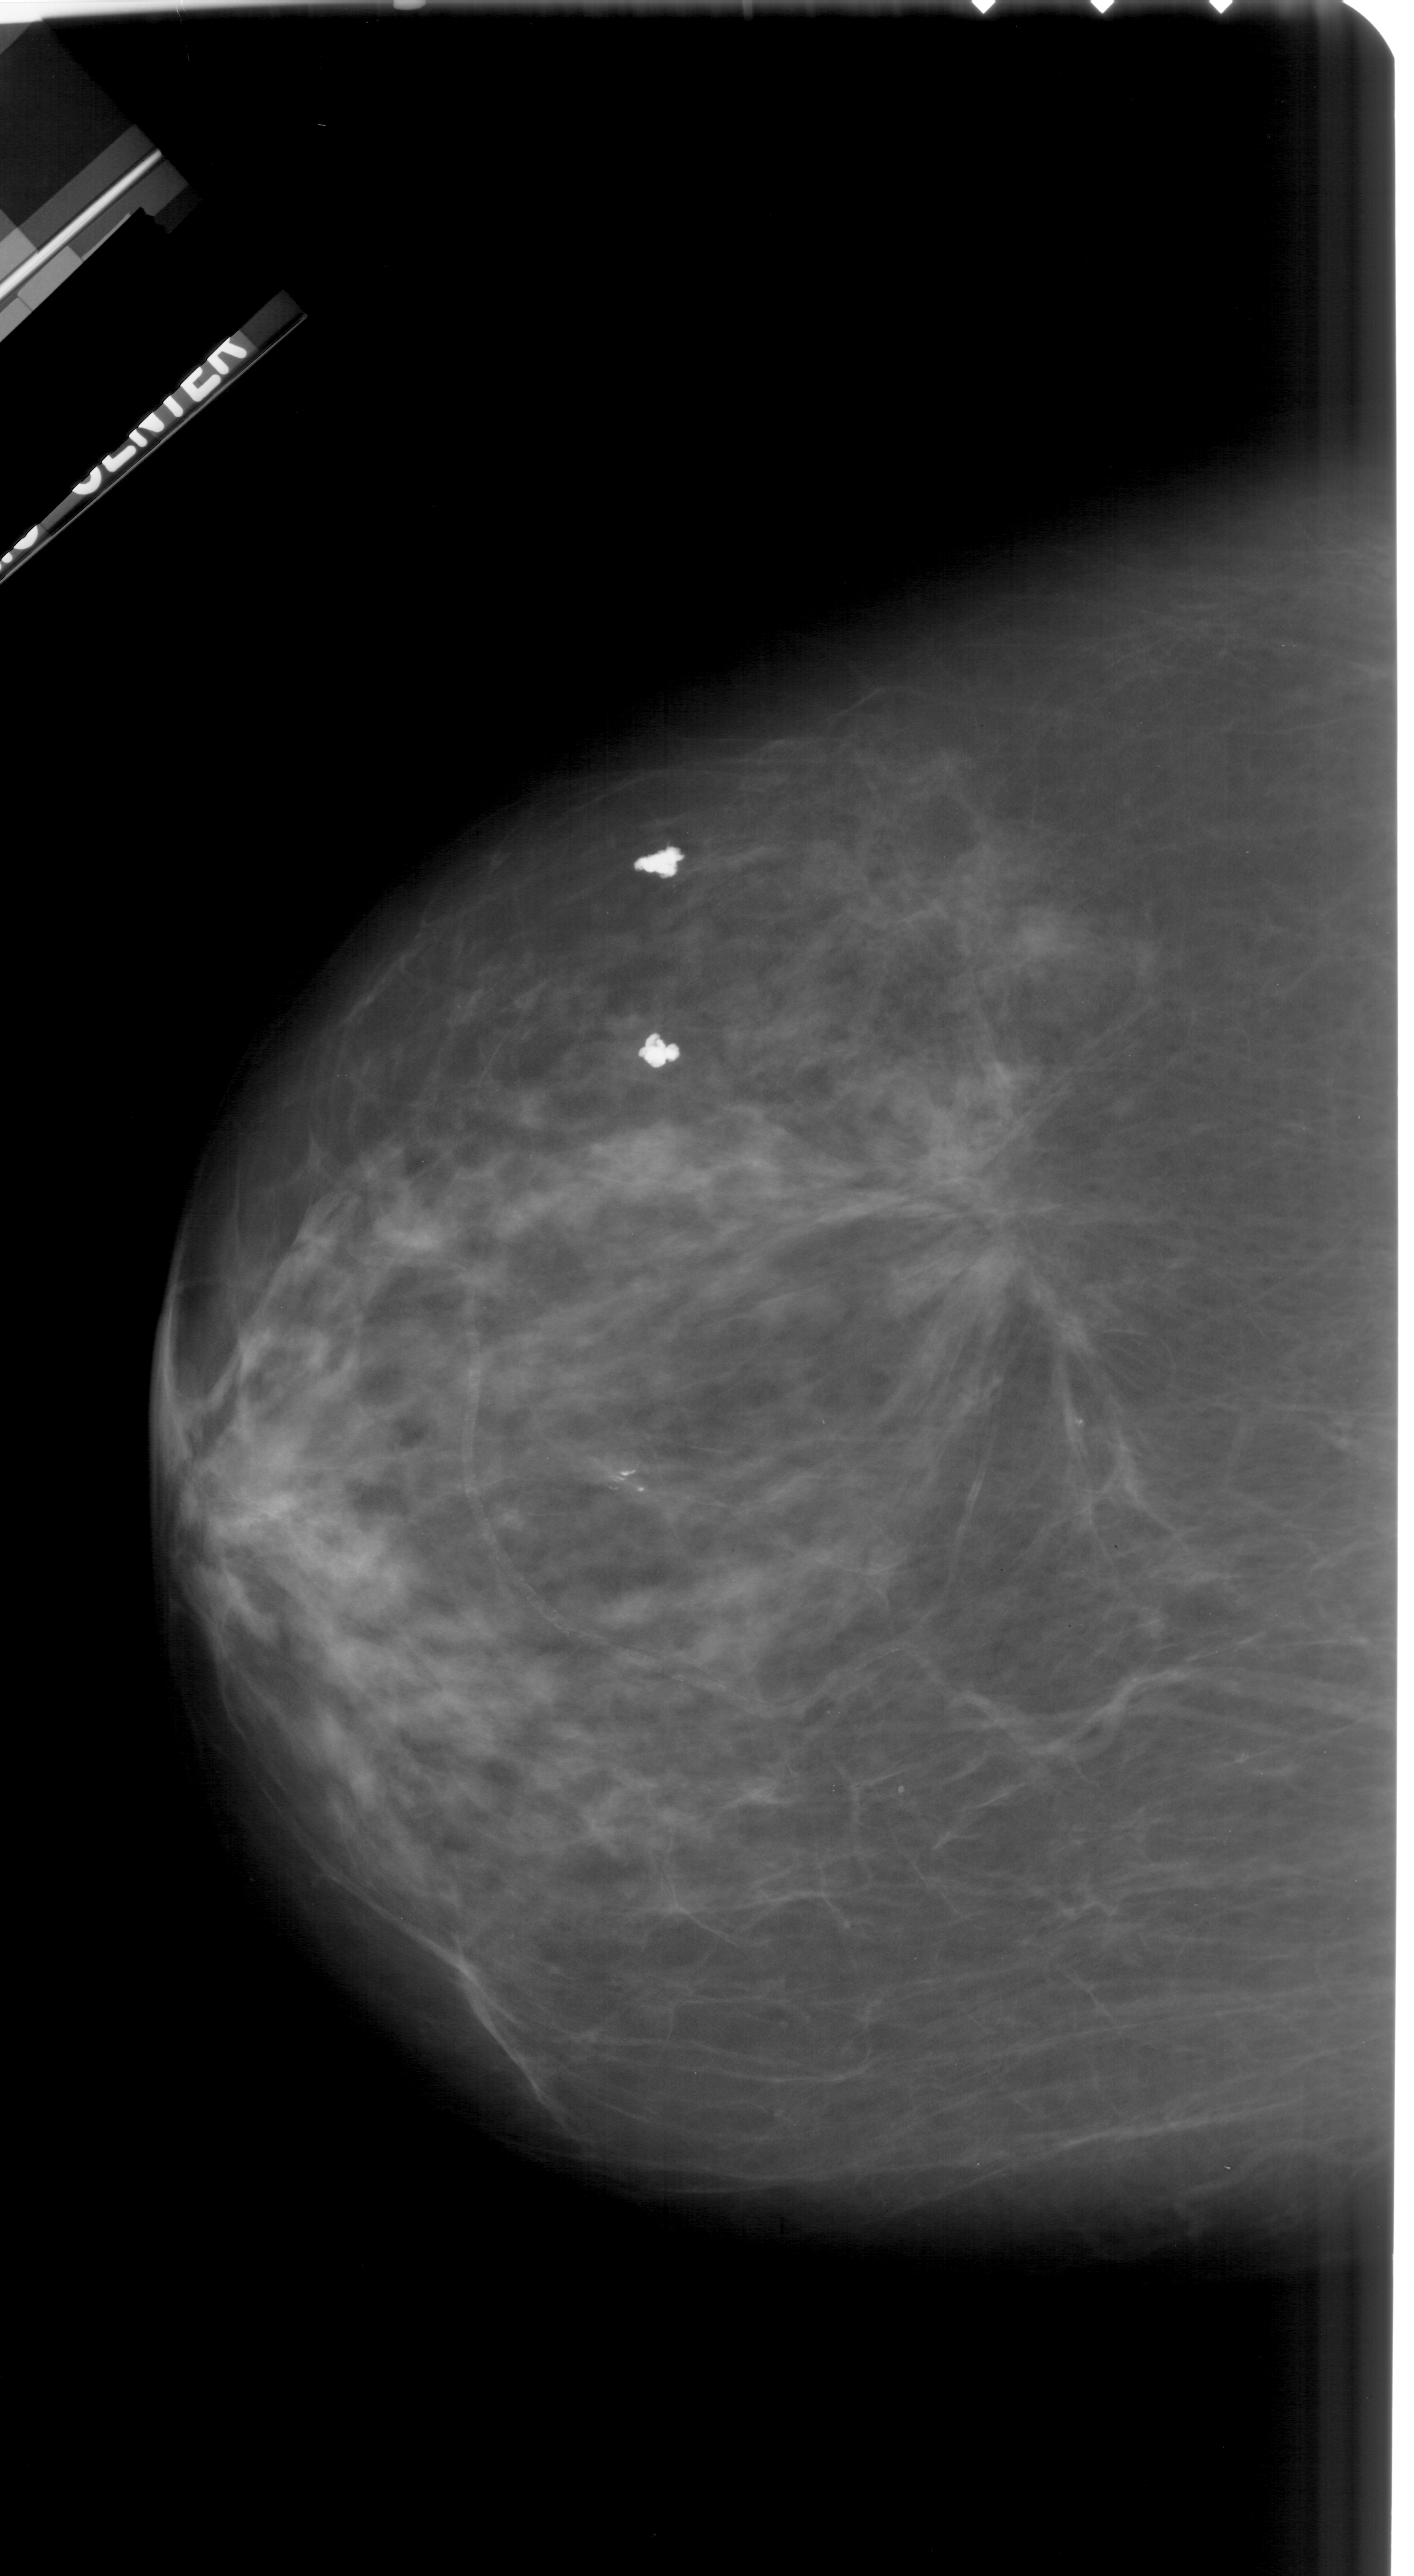
Mammogram (digitized film). Left breast. CC view. Breast composition: scattered fibroglandular densities (BI-RADS density category 2 of 4). 1414 × 2576 image matrix.
Expert-marked regions of interest on this image (one box per marked abnormality):
- mass, shape architectural distortion, margins spiculated; BI-RADS assessment category 5; pathology result (as recorded, not read from the image): malignant: bounding box (x1, y1, x2, y2) in pixels: (870, 1087, 1099, 1342)